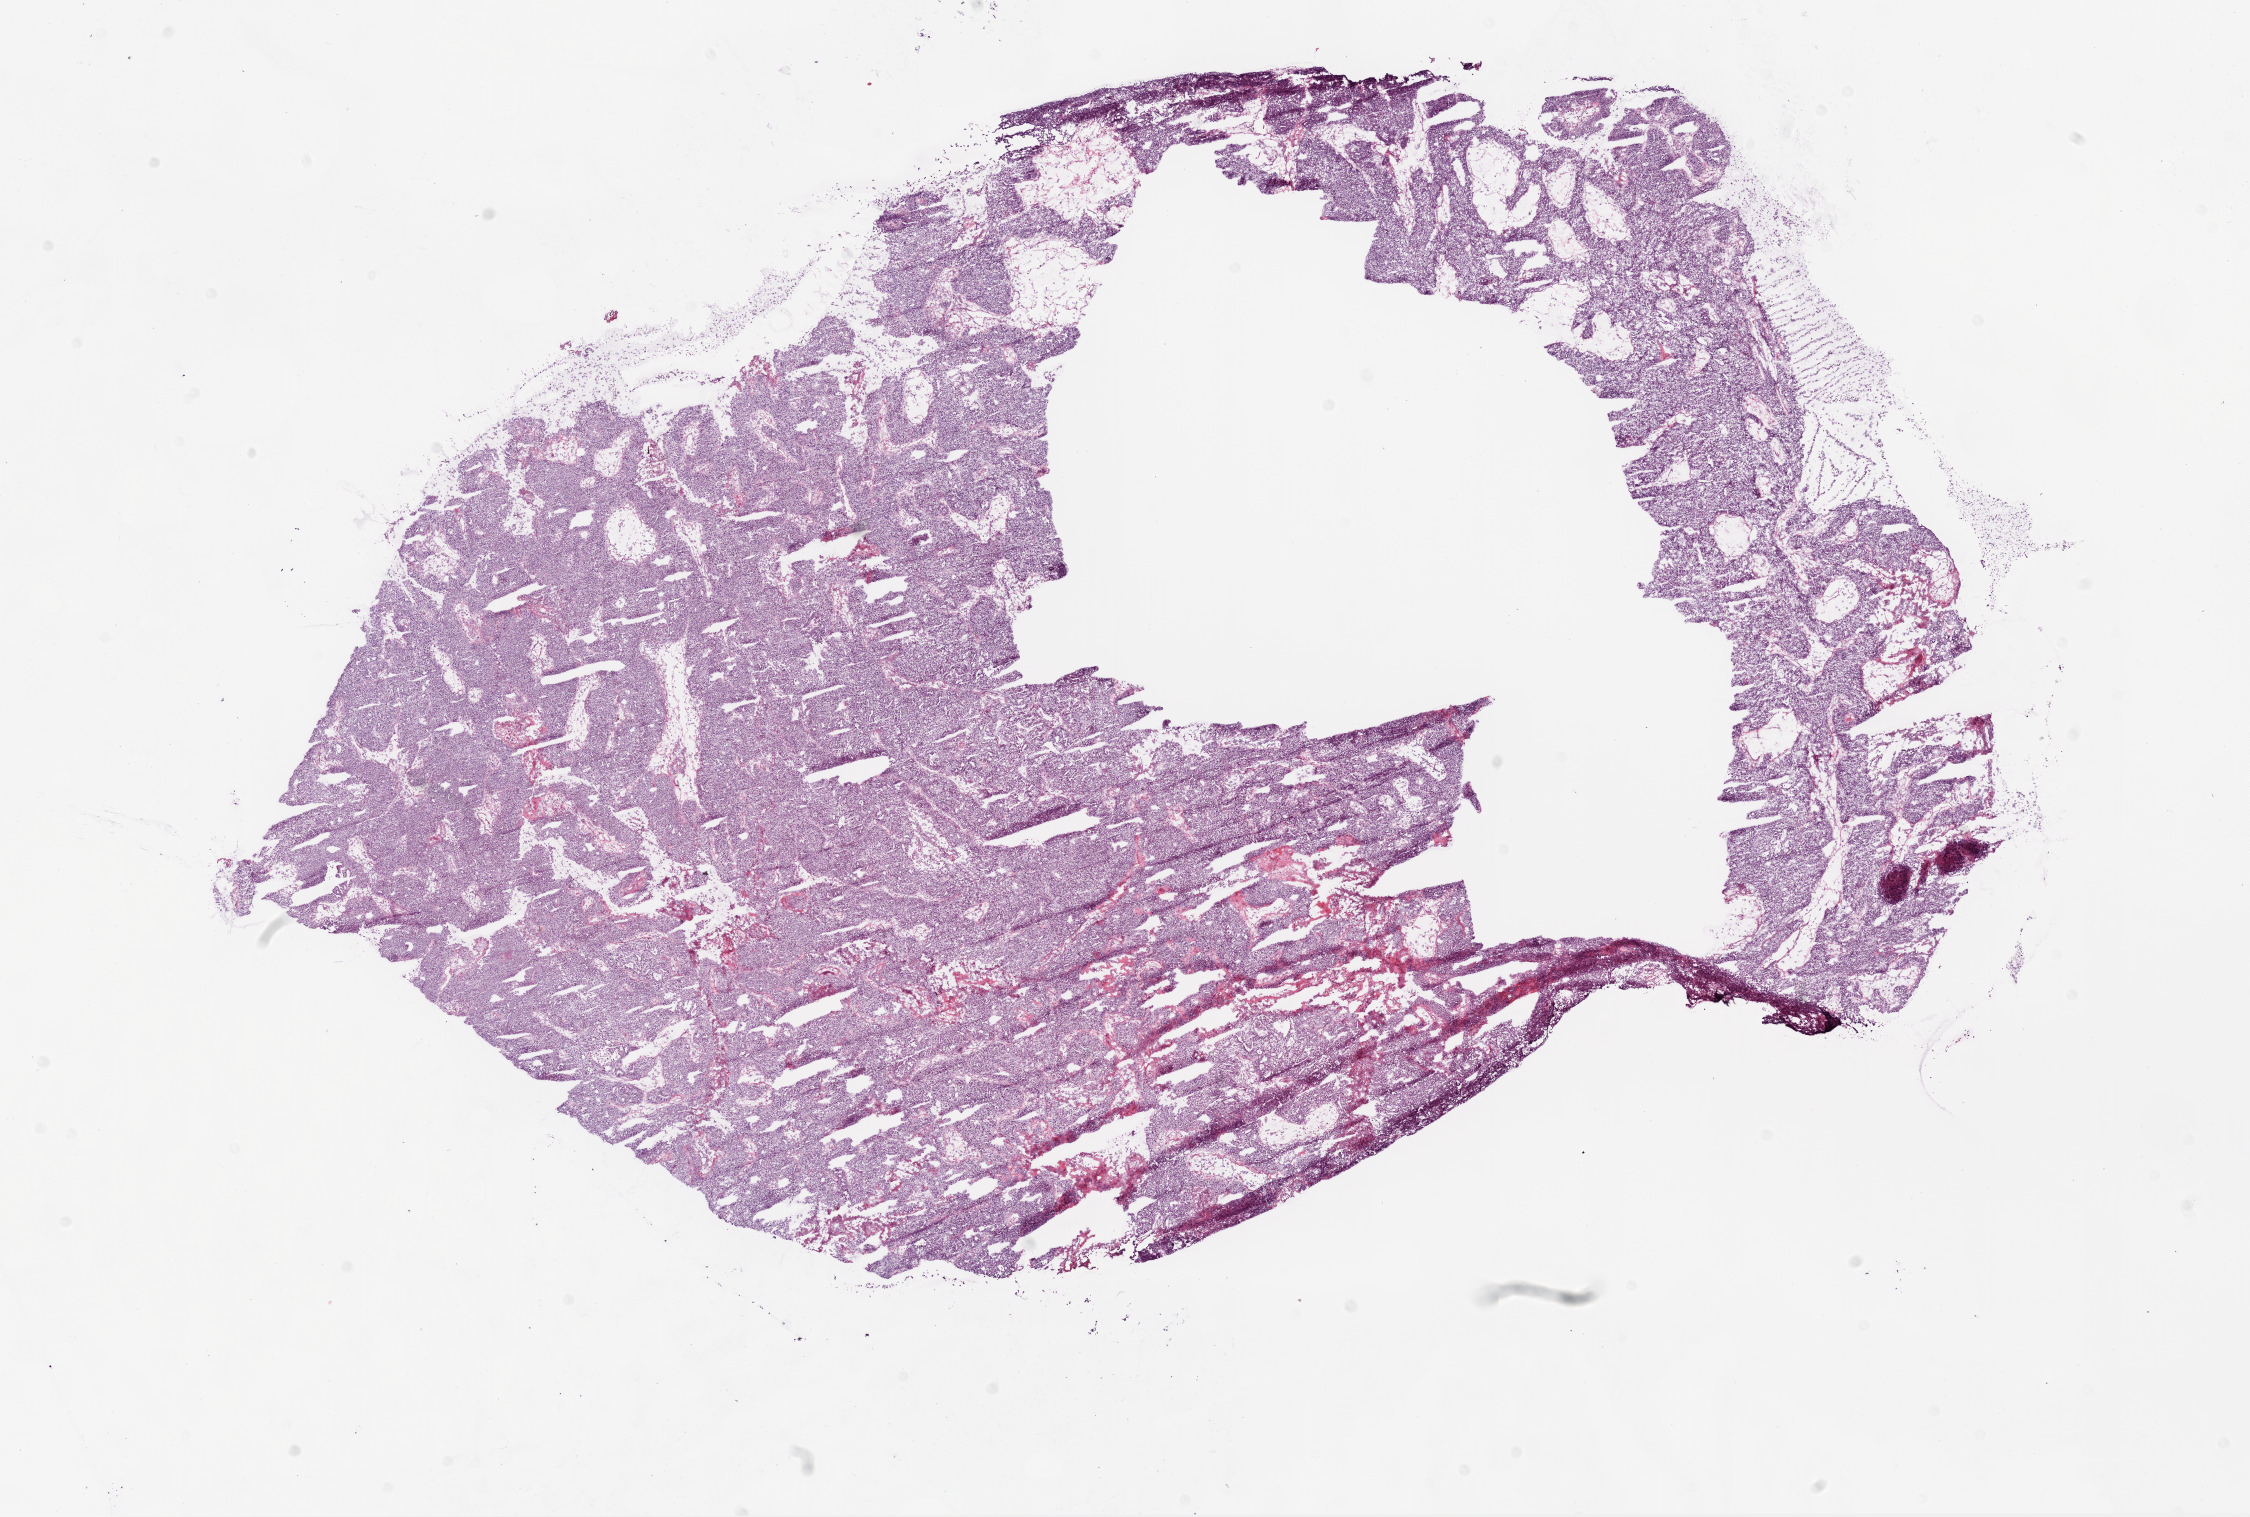
Whole-slide histology image, H&E, shown as a low-resolution overview of the whole scanned area (about 18.1 x 12.2 mm). Frozen section from the bottom of the tissue portion. Ovary, primary tumour sample. Female, age 55 years at initial diagnosis. Histologic grade: G3 (poorly differentiated). Slide review estimates, as recorded: tumour cells 94%, tumour nuclei 95%, normal cells 0%, stromal cells 5%, necrosis 1%.
FIGO stage: IB. Histologic diagnosis: Serous cystadenocarcinoma, NOS. Laterality: bilateral.